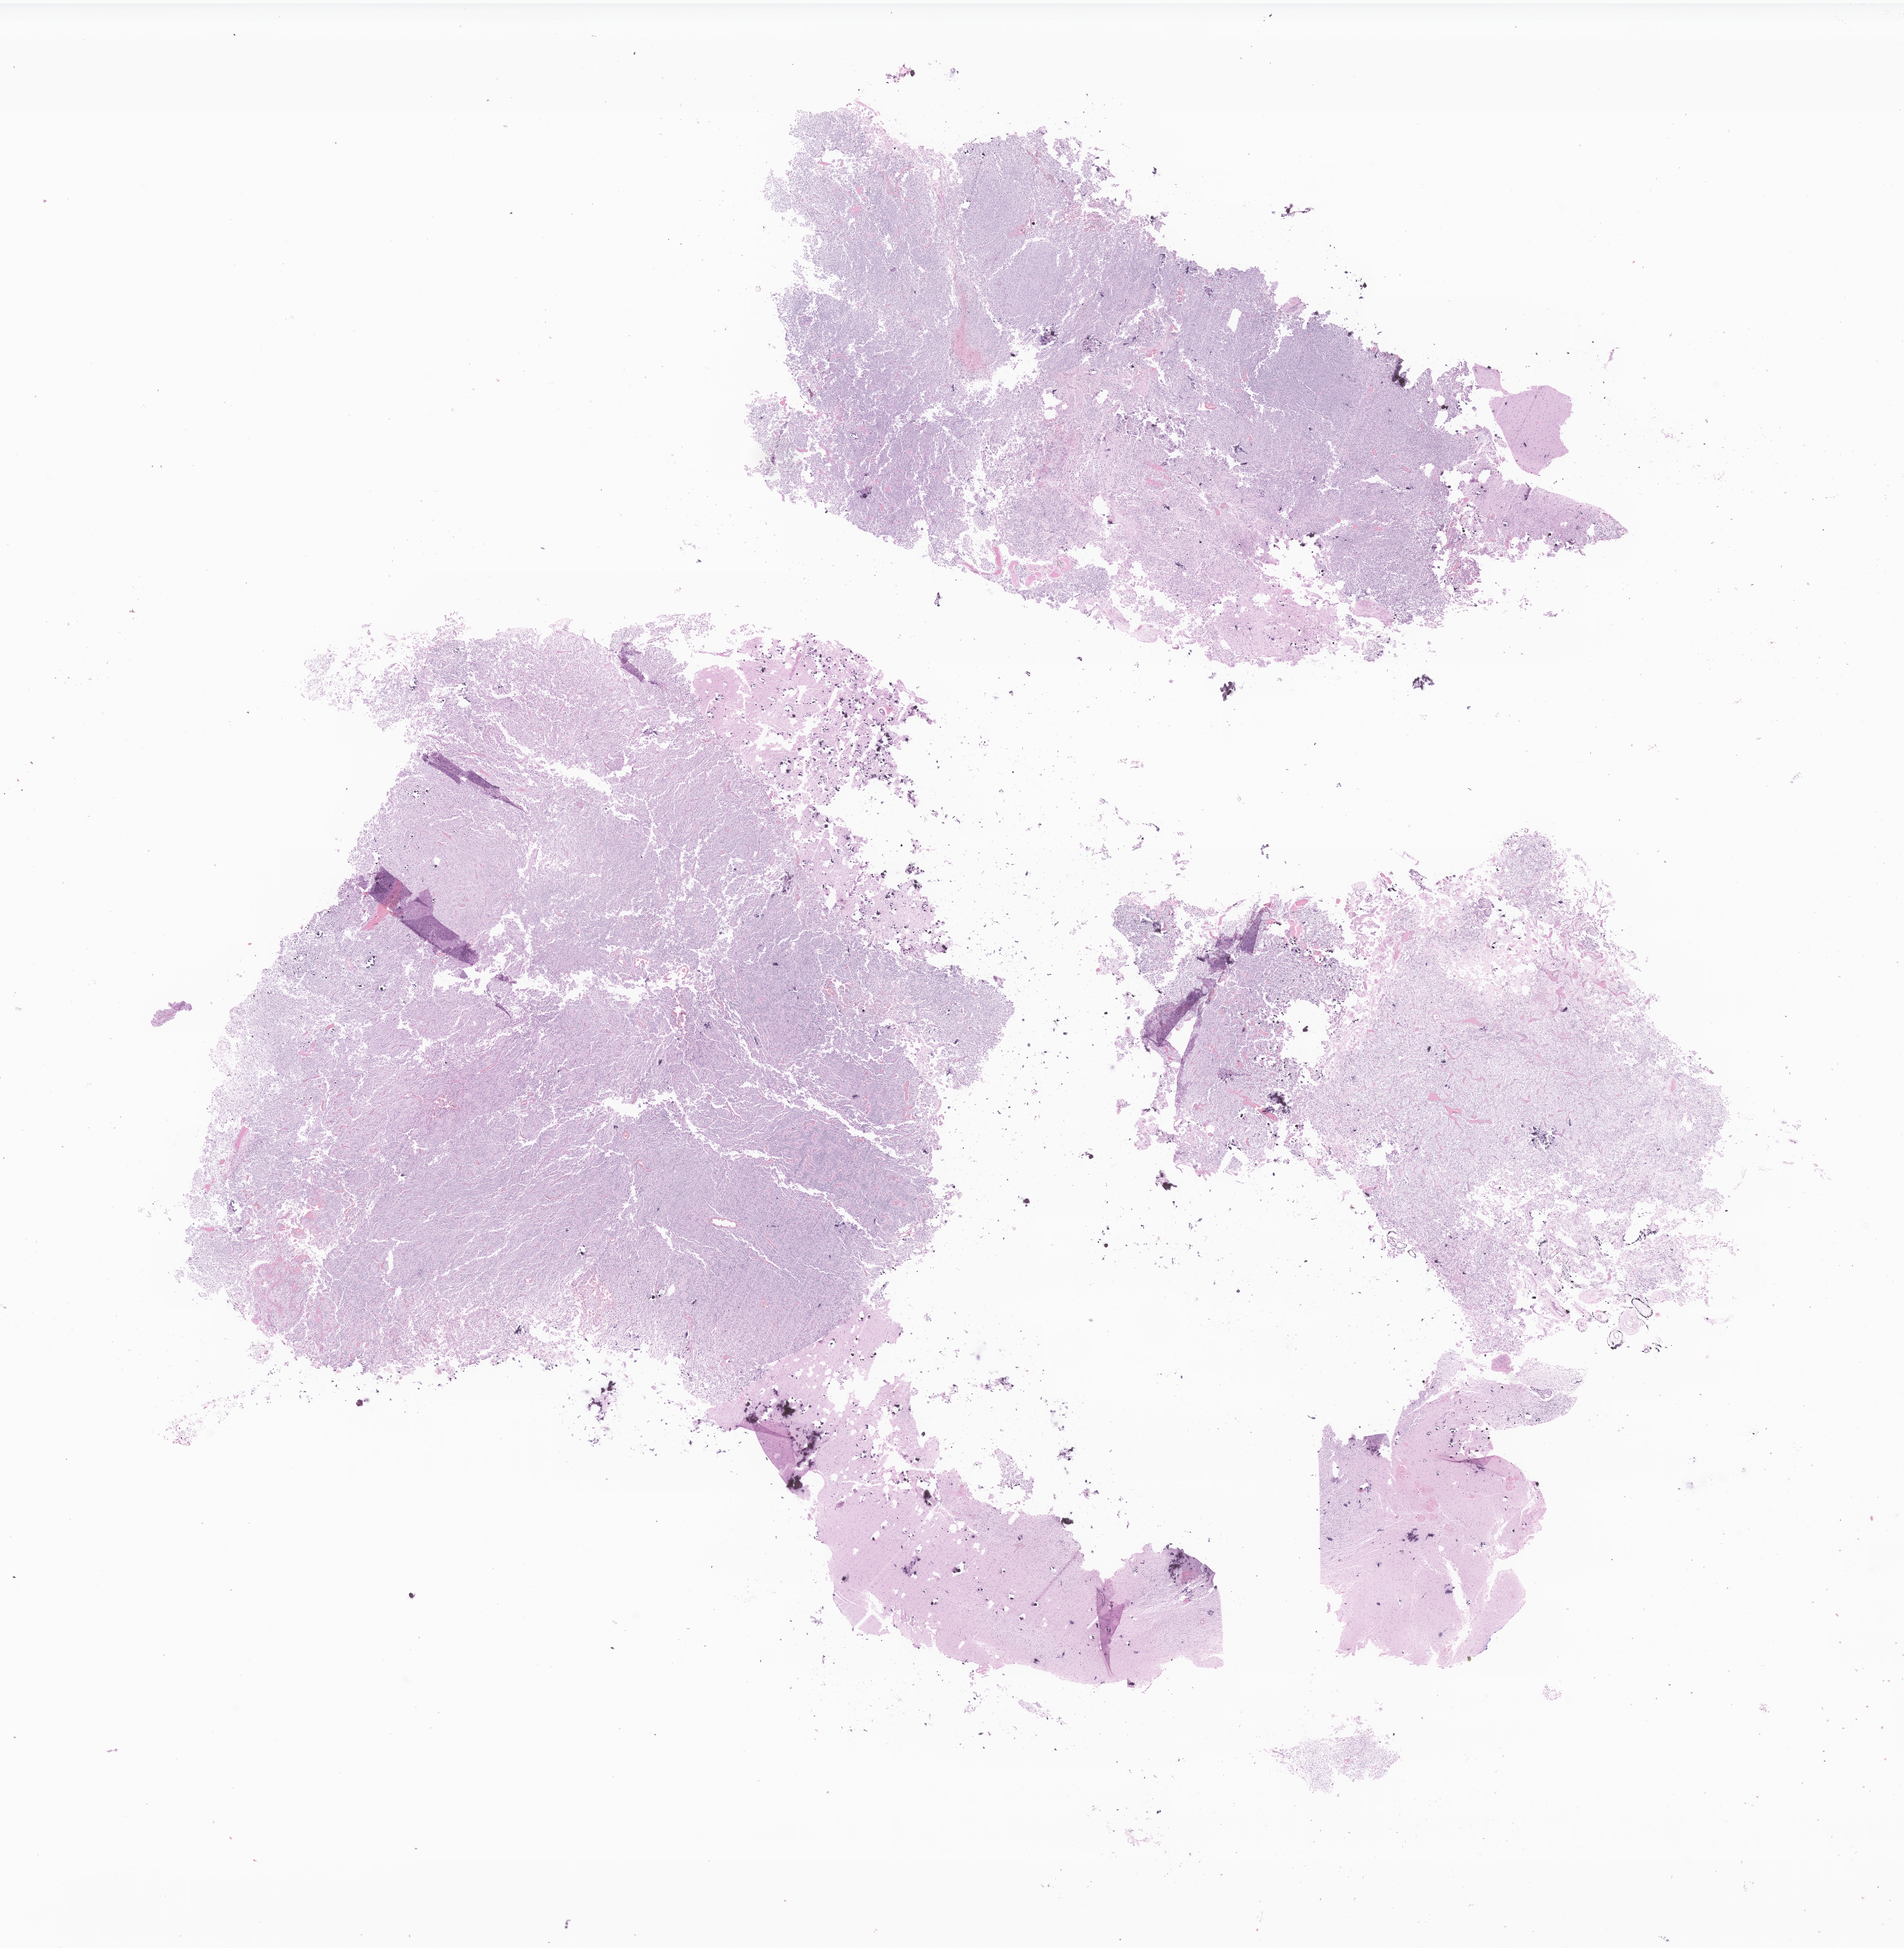
Whole-slide image, hematoxylin and eosin (H&E) stain of tumor tissue from the brain — a low-resolution overview of the entire scanned area, about 22.1 x 22.6 mm, formalin-fixed, paraffin-embedded (FFPE) tissue. Male patient, age 244 months.
Recorded diagnosis: Glioma, malignant.